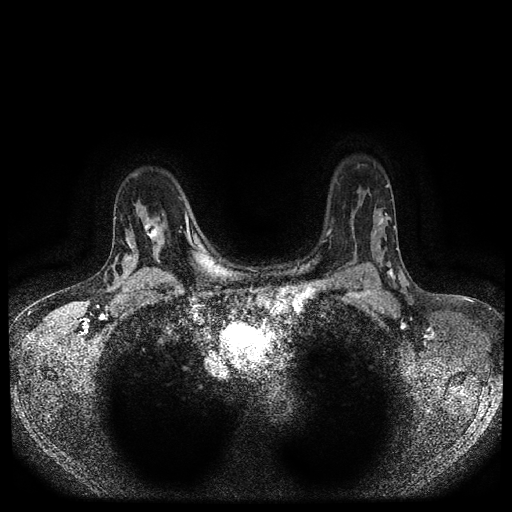
Breast MRI (dynamic contrast-enhanced, multi-phase), one axial slice; position 74 of 116 along the scan axis; dynamic contrast-enhanced series, time point 2 of 5 at this slice position (early post-contrast); 1.5 T; TE 2.6 ms, TR 5.4 ms; 2 mm slice thickness; 512 × 512 image matrix, field of view 340 × 340 mm. Female patient, age 47 years.
Annotated regions visible in this slice (semi-automatically segmented with operator editing):
- breast lesion (labelled 'tumour' in the annotation; benign lesions carry a separate 'benign' label): bounding box (x1, y1, x2, y2) in pixels: (143, 217, 161, 243)